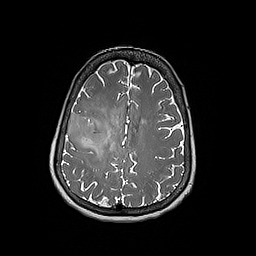
Brain MRI from a brain-tumour surgery series, one axial slice; slice 70 of 192 in the series (ordered by position); 1 mm slice thickness; 256 × 256 image matrix, field of view 250 × 250 mm. Case-level facts recorded for this patient, not image findings: histopathology: Oligodendroglioma; WHO grade: 3; IDH mutation: yes.
Annotated regions visible in this slice (expert manual segmentation):
- tumour: bounding box (x1, y1, x2, y2) in pixels: (67, 112, 110, 149)